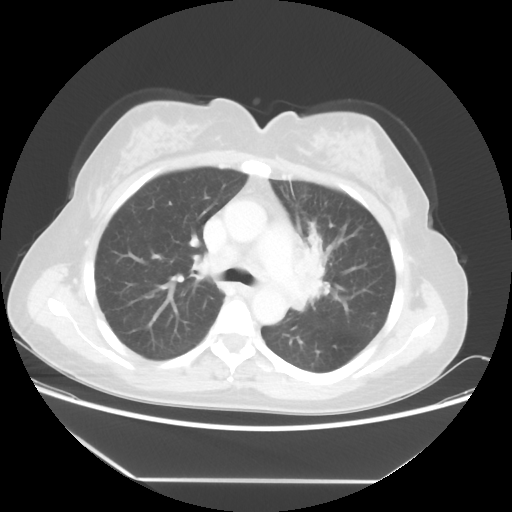
Chest CT, one axial slice; slice 34 of 52 in the series (ordered by position); reconstruction kernel STANDARD; 100 kVp; lung window (W 1500 / L -600 HU); 512 × 512 image matrix, field of view 390 × 390 mm. Patient: female, 50 years. From the clinical record (not read from this slice): clinical TNM (as recorded): T2 N3 M0.
Outlined on this slice (bounding box drawn by a radiologist):
- lung tumour (recorded histology: adenocarcinoma): bounding box [x1, y1, x2, y2] px = [291, 233, 341, 328]